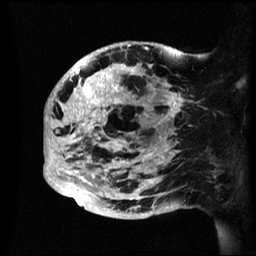
Breast MRI (dynamic contrast-enhanced), one sagittal slice; position 20 of 60 along the scan axis; dynamic contrast-enhanced series, image 2 of 3 at this slice position (ordered by acquisition); 1.5 T; TE 4.2 ms, TR 8.4 ms; 256 × 256 image matrix, field of view 230 × 230 mm. Female patient, age 48 years.
Structures marked on this image (semi-automatically segmented with operator editing):
- analysis volume of interest (the breast-tissue region the enhancement analysis was run in; not a lesion): bounding box (x1, y1, x2, y2) in pixels: (44, 42, 195, 219)
- tumour enhancement mask (voxels above the 70 % enhancement threshold inside the analysis volume of interest): (44, 42, 183, 207)